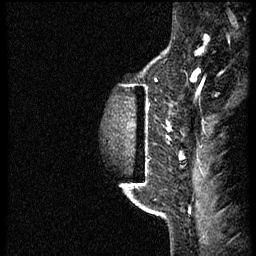
Breast MRI (dynamic contrast-enhanced), one sagittal slice; slice 48 of 56 in the series (ordered by position); dynamic contrast-enhanced study with each time point stored as its own series, time point 2 of 3 at this slice position (early post-contrast, ordered by acquisition time); 1.5 T; TE 4.2 ms, TR 21.3 ms; 2 mm slice thickness; 256 × 256 image matrix, field of view 200 × 200 mm. Patient: female, 41 years. Case-level facts recorded for this patient, not image findings: setting: breast cancer imaged before/during neoadjuvant chemotherapy; receptor status: HER2-positive.
Structures marked on this image (semi-automatic segmentation, software-assisted and operator-edited):
- analysis volume of interest (the breast-tissue region the enhancement analysis was run in; not a lesion): box from (x=124, y=73) to (x=177, y=205) px
- tumour enhancement mask (voxels above the 100 % enhancement threshold inside the analysis volume of interest): (x=146, y=107)–(x=171, y=138)